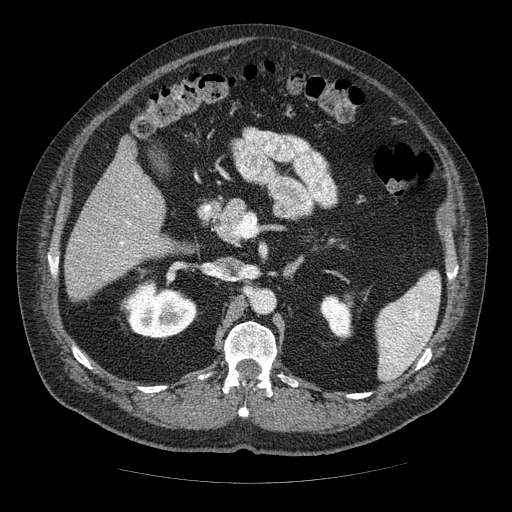
Contrast-enhanced abdominal CT (liver protocol), one axial slice. Position 22 of 85 along the scan axis. Reconstruction kernel STANDARD. Soft-tissue window (W 400 / L 40 HU). 512 × 512 image matrix, field of view 420 × 420 mm. From the clinical record (not read from this slice): diagnosis: hepatocellular carcinoma (patient treated with transarterial chemoembolisation; whether this scan precedes or follows treatment is not stated here); TNM stage (as recorded): Stage-IIIA; Child-Pugh class: A; tumour nodularity: multinodular; tumour size: 7 cm.
Outlined on this slice (semi-automatically segmented with operator editing):
- liver parenchyma outside the tumour (the mass and vessels are separate outlines, so this box may not span the whole liver): bounding box (x1, y1, x2, y2) in pixels: (64, 138, 170, 300)
- liver vessels: (120, 195, 139, 257)